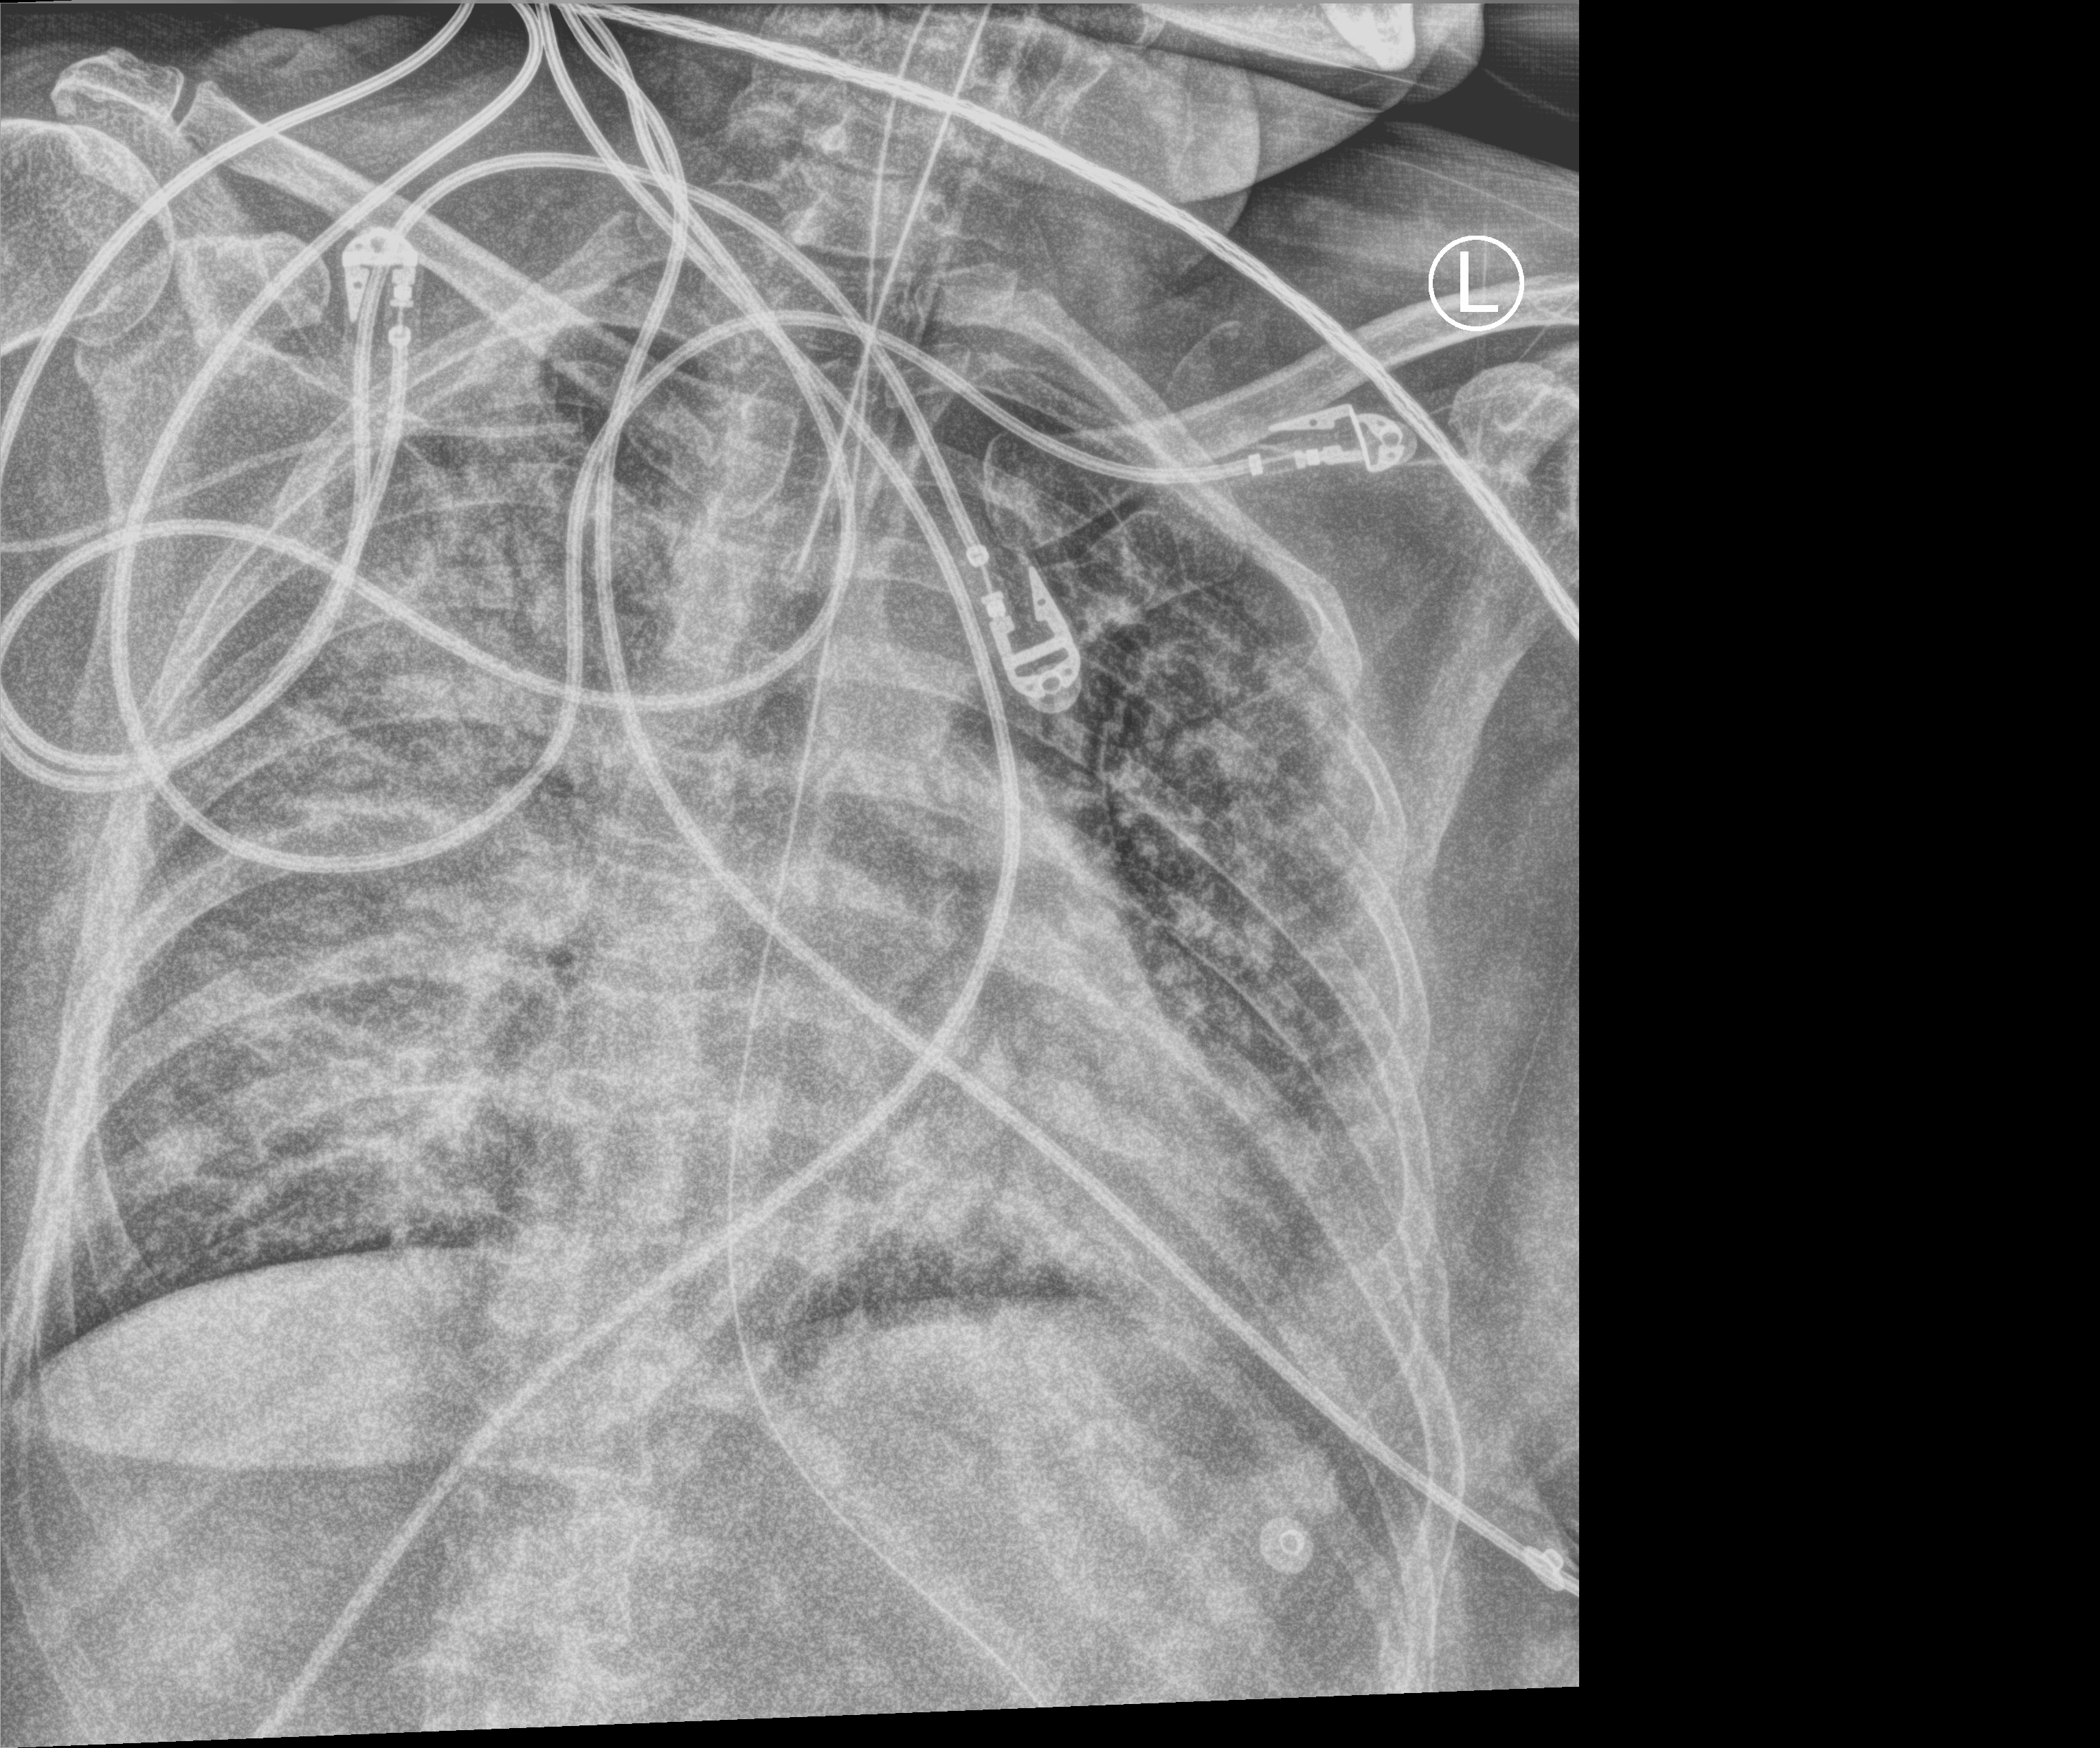
Portable chest radiograph, anteroposterior (AP) projection. Patient hospitalised with COVID-19; female, aged 18–59 years.
Hospital-stay facts (about this admission, not read from this image; timing relative to this image not recorded): admitted to intensive care during this hospital stay: yes; mechanically ventilated during this hospital stay: yes; smoking status (admission record): never.